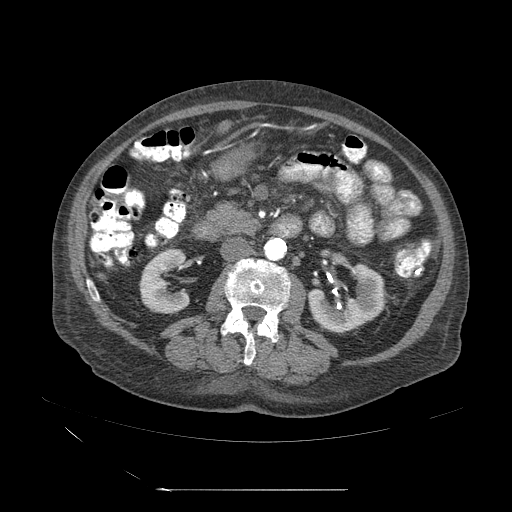
Contrast-enhanced abdominal CT (liver protocol), one axial slice; position 4 of 71 along the scan axis; 120 kVp; soft-tissue window (W 400 / L 40 HU); 2.5 mm slice thickness; 512 × 512 image matrix. Case-level facts recorded for this patient, not image findings: diagnosis: hepatocellular carcinoma (patient treated with transarterial chemoembolisation; whether this scan precedes or follows treatment is not stated here); TNM stage (as recorded): Stage-II; Child-Pugh class: A.
Structures marked on this image (semi-automatically segmented with operator editing):
- abdominal aorta: bounding box <264,237,287,263> (left, top, right, bottom; pixels)